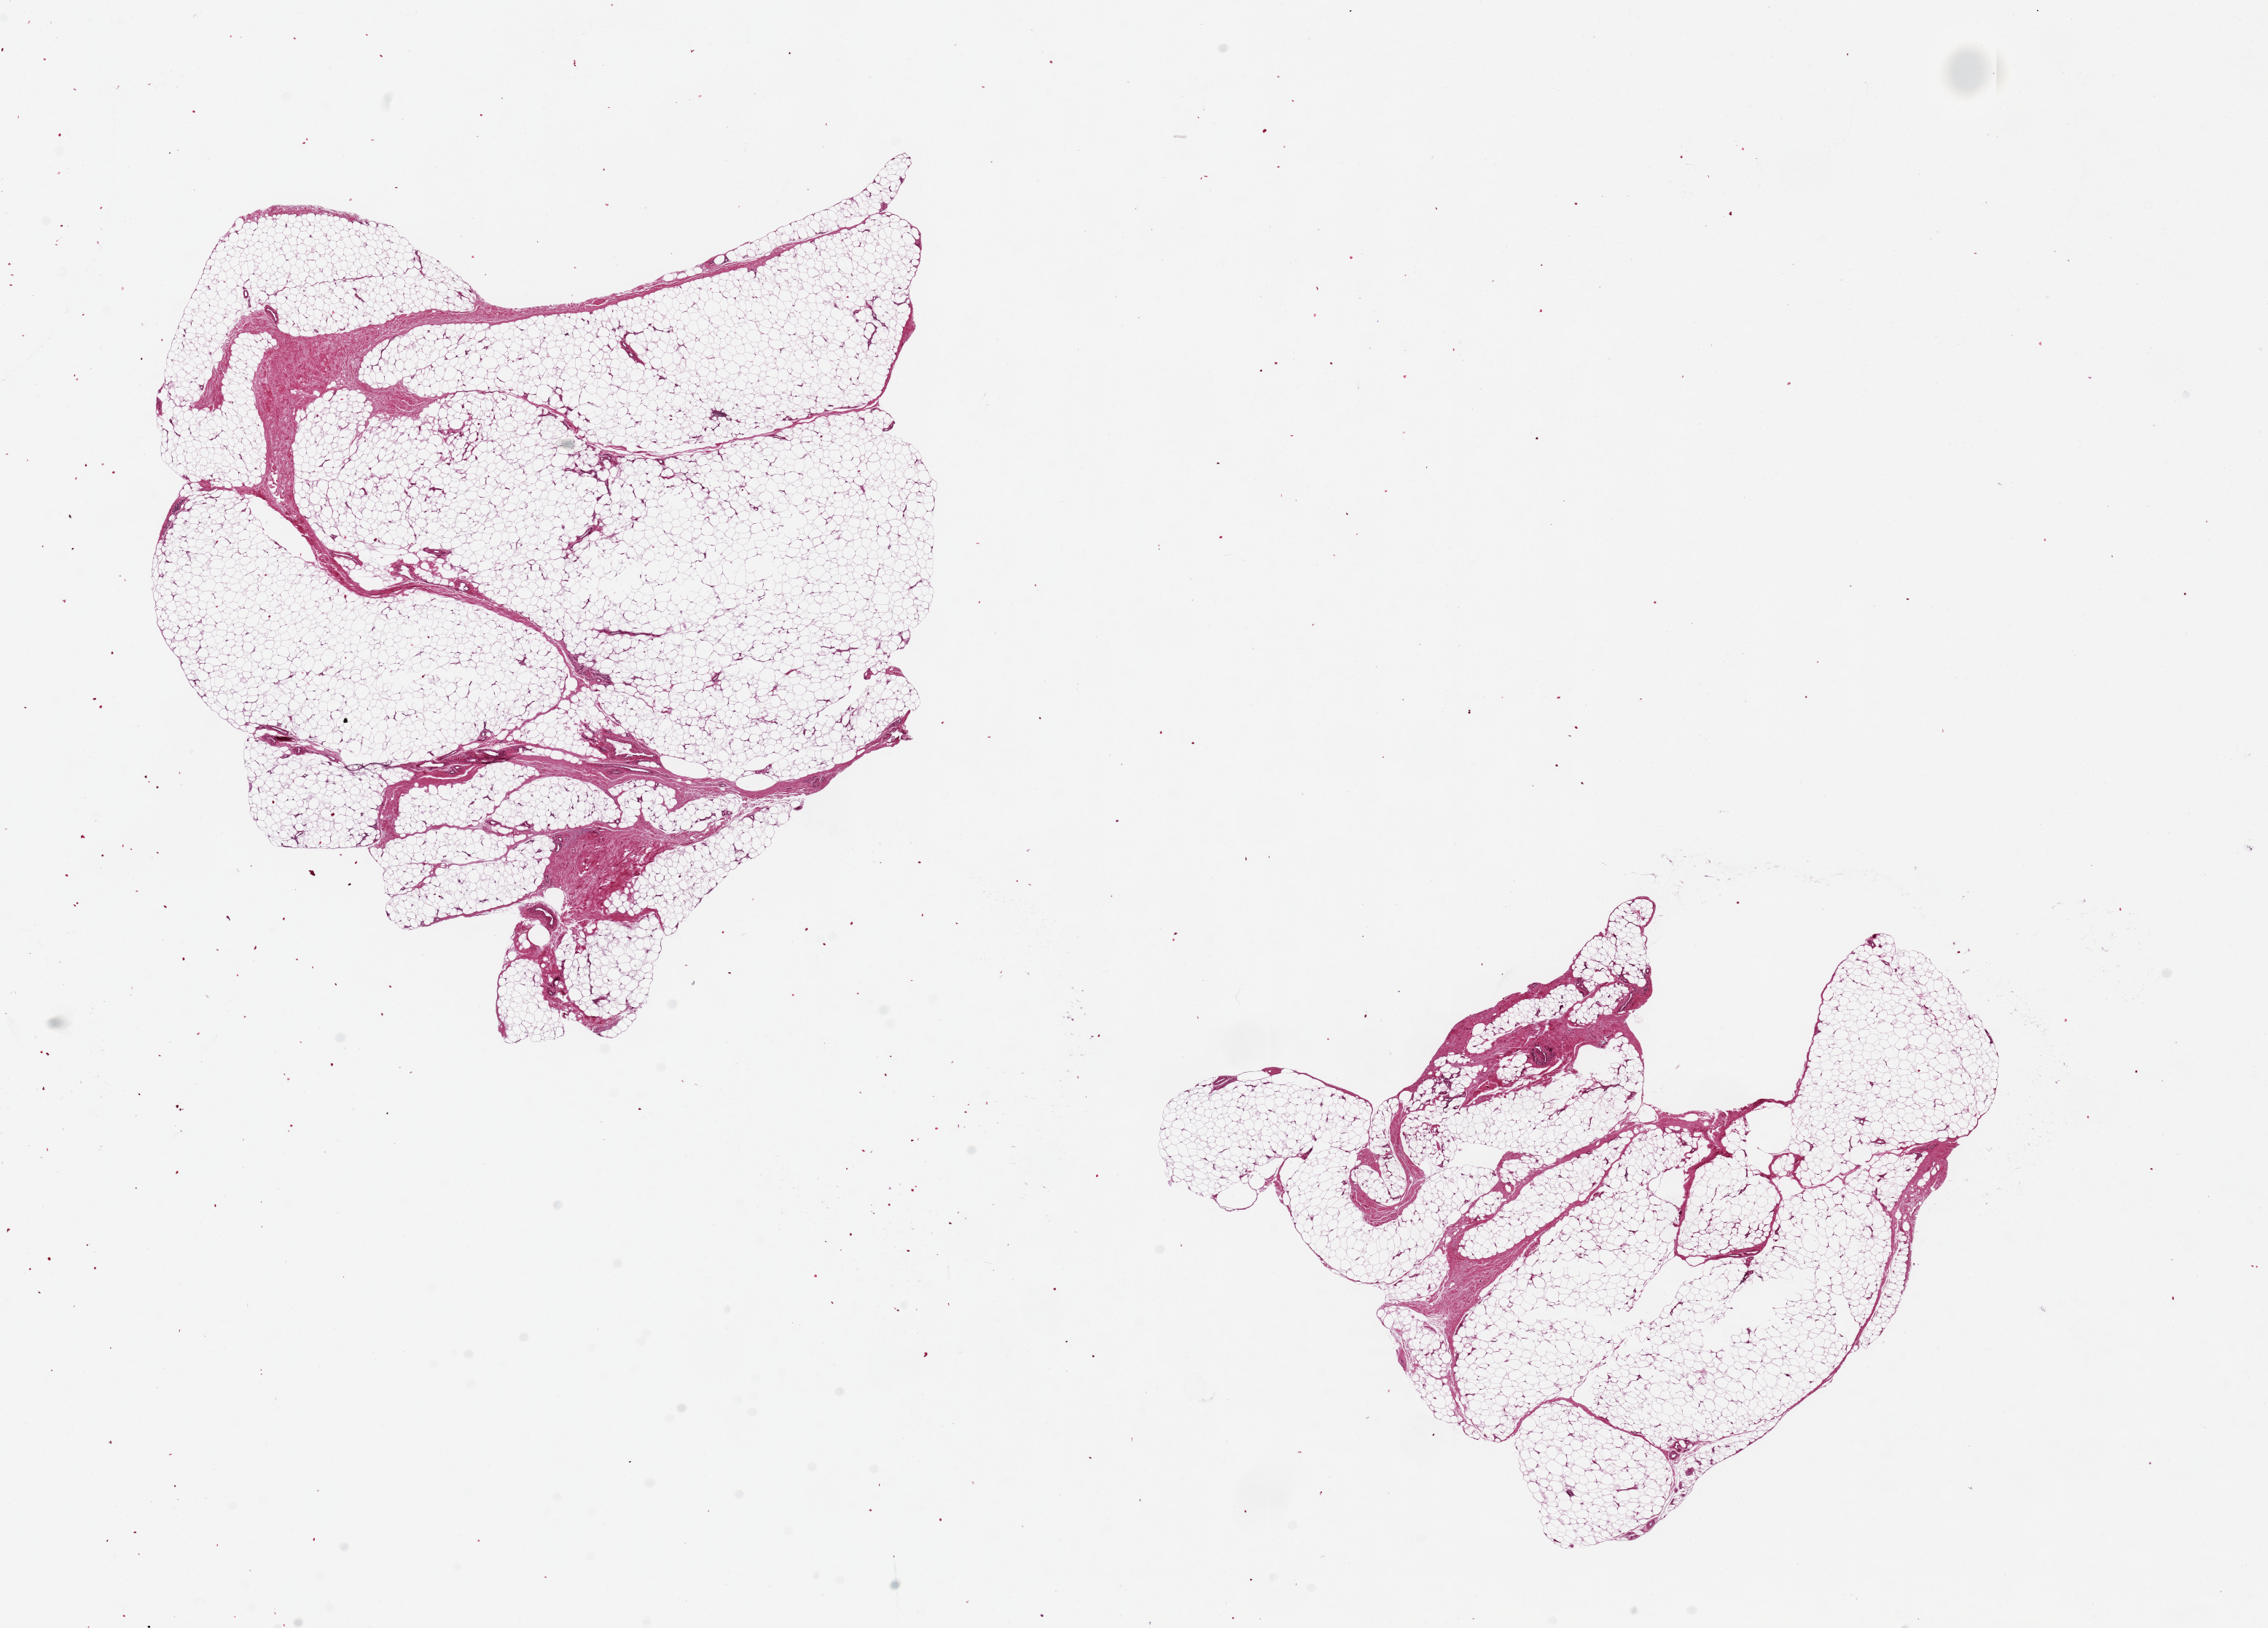
Digitized haematoxylin and eosin-stained section, brightfield — a low-resolution overview of the entire scanned area, about 24.6 x 17.7 mm (from a 20x scan); PAXgene-fixed, paraffin-embedded tissue; section of adipose tissue (target tissue); tissue donor sample. Donor: male.
Pathologist's review note for this sample: 2 pieces, 9x9 & 7x7mm; minimal artifacts.